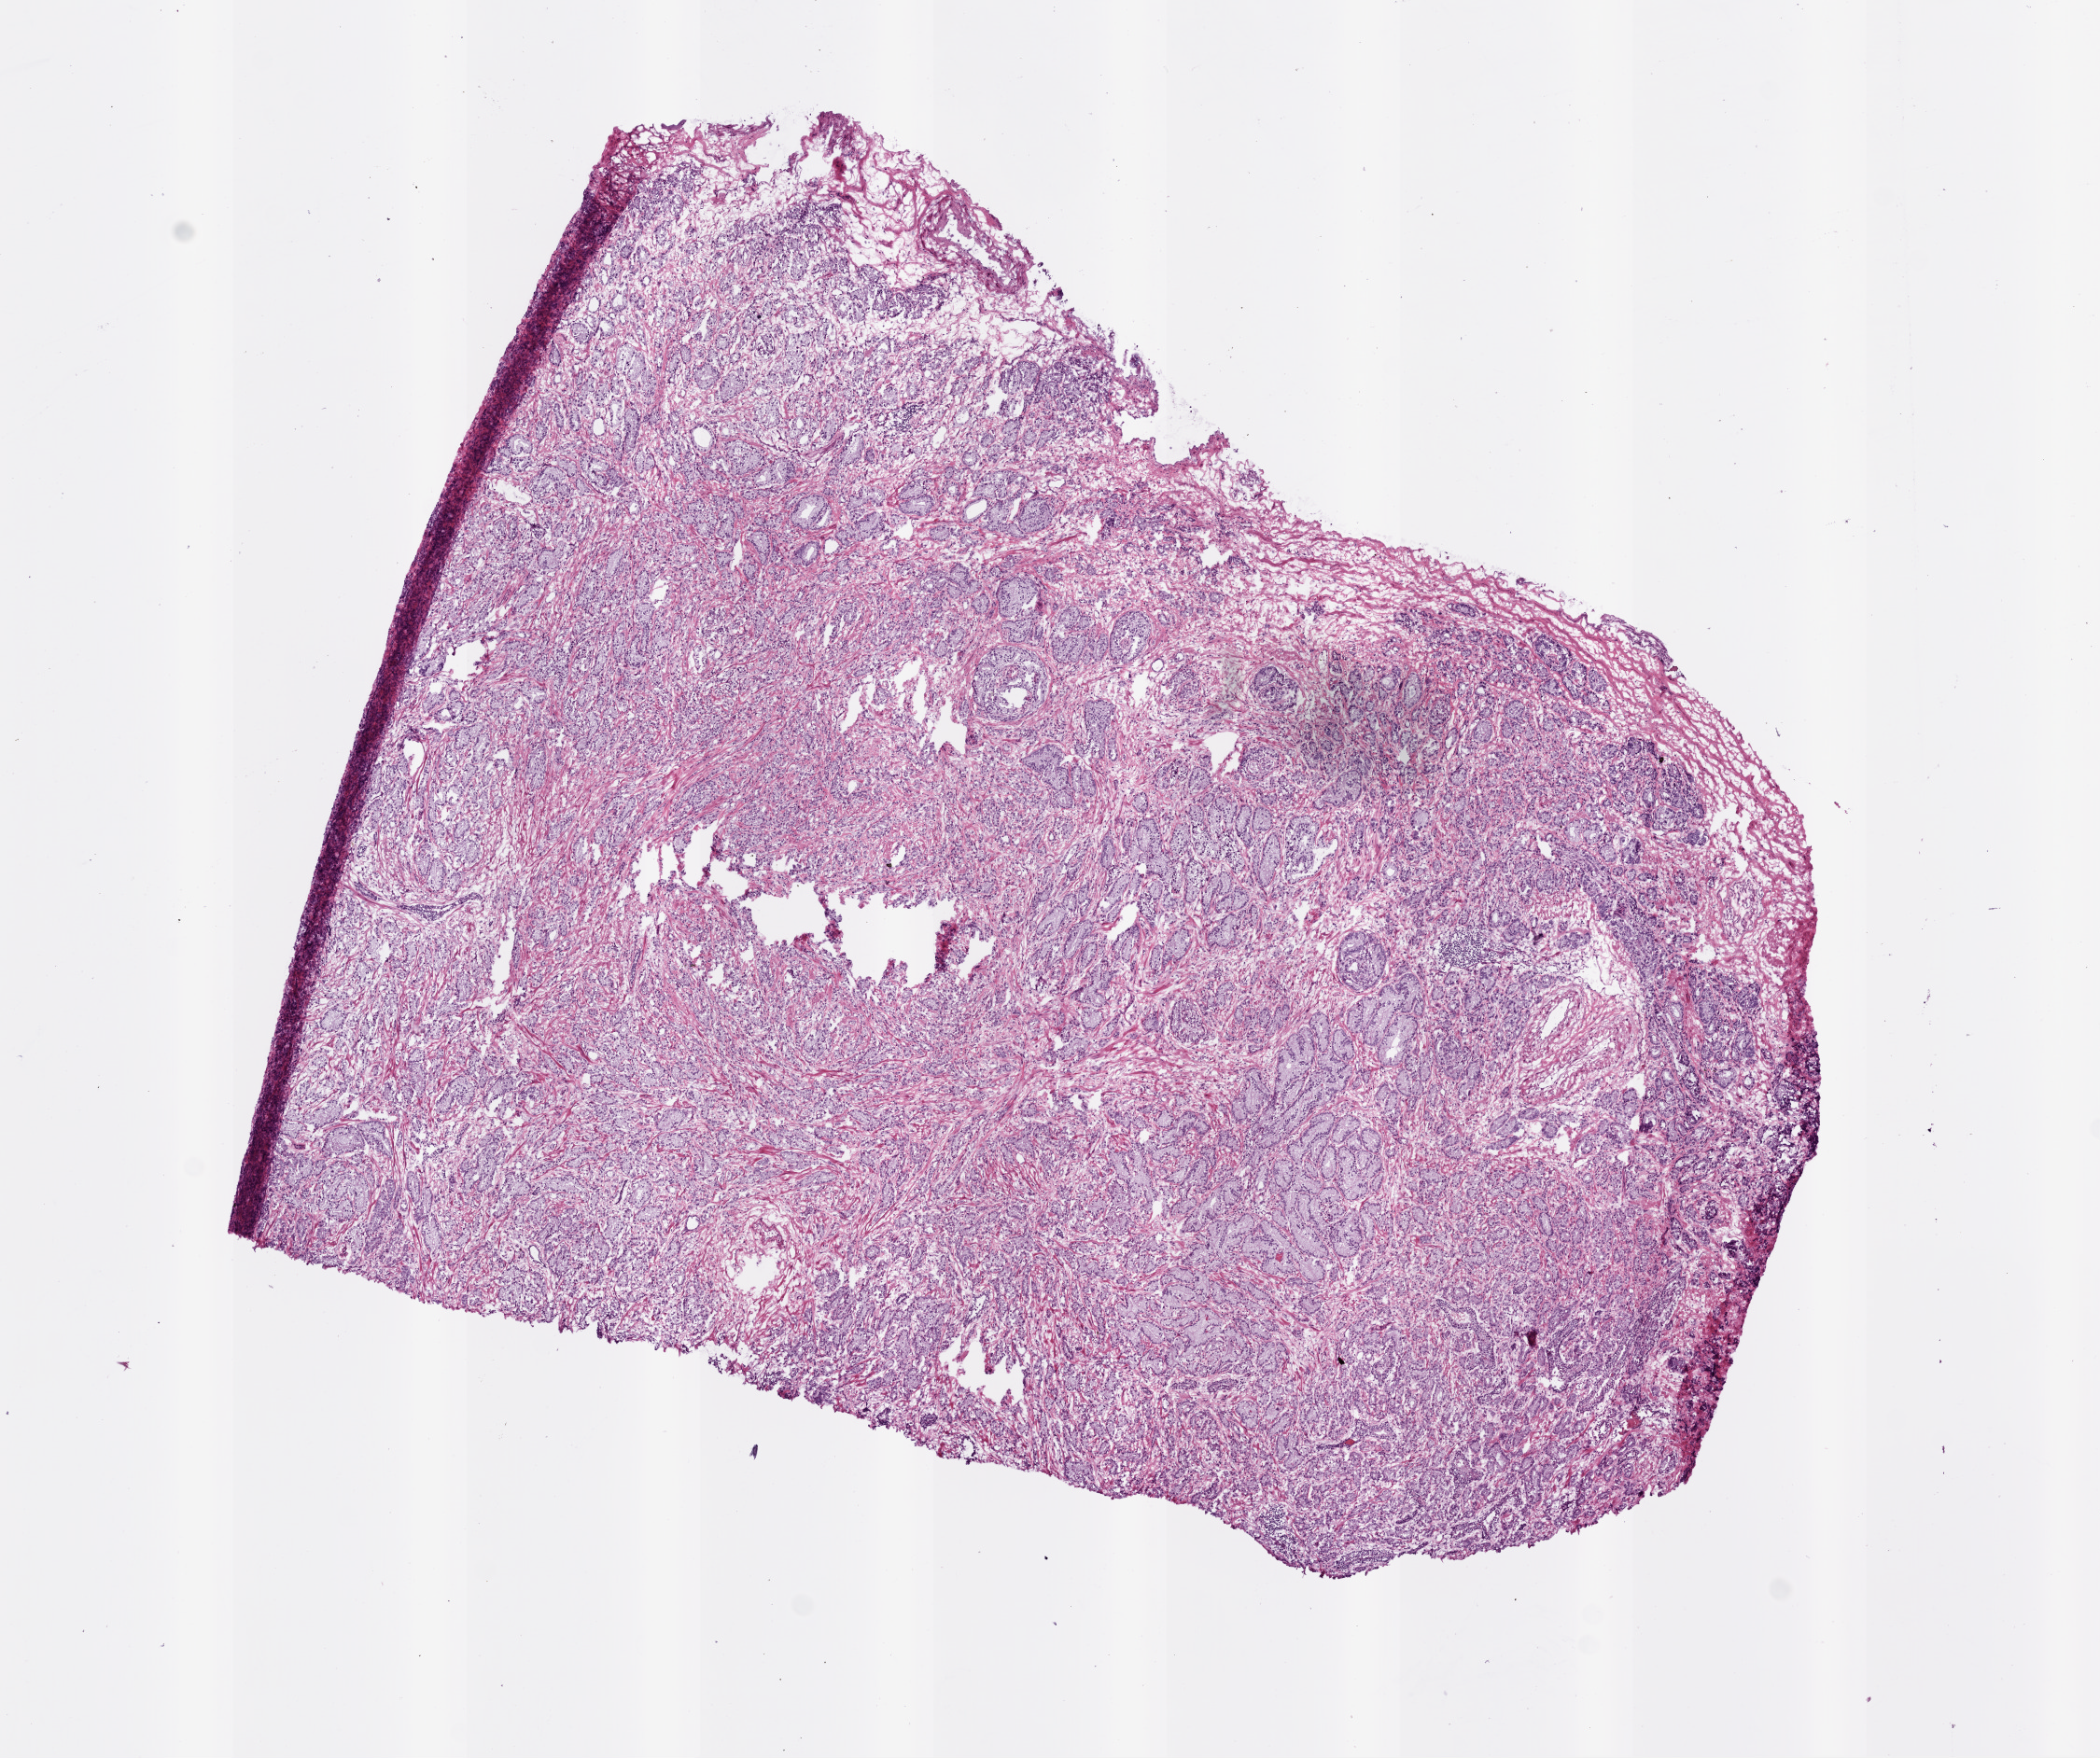
H&E whole-slide image — shown as a low-resolution overview of the whole scanned area (about 9.0 x 7.6 mm), frozen section from the bottom of the tissue portion, primary tumour sample from the prostate. Male, age 65 years at initial diagnosis. Gleason score: 7 (3+4). Composition of this section per pathologist review: tumour cells 90%, tumour nuclei 85%, normal cells 2%, stromal cells 8%, necrosis 0%. Infiltration values recorded for this section: lymphocyte infiltration 0%, monocyte infiltration 0%, neutrophil infiltration 0%.
Lymph nodes positive (case pathology): 0 of 8 examined. Histologic diagnosis: Acinar cell carcinoma (prostate gland).